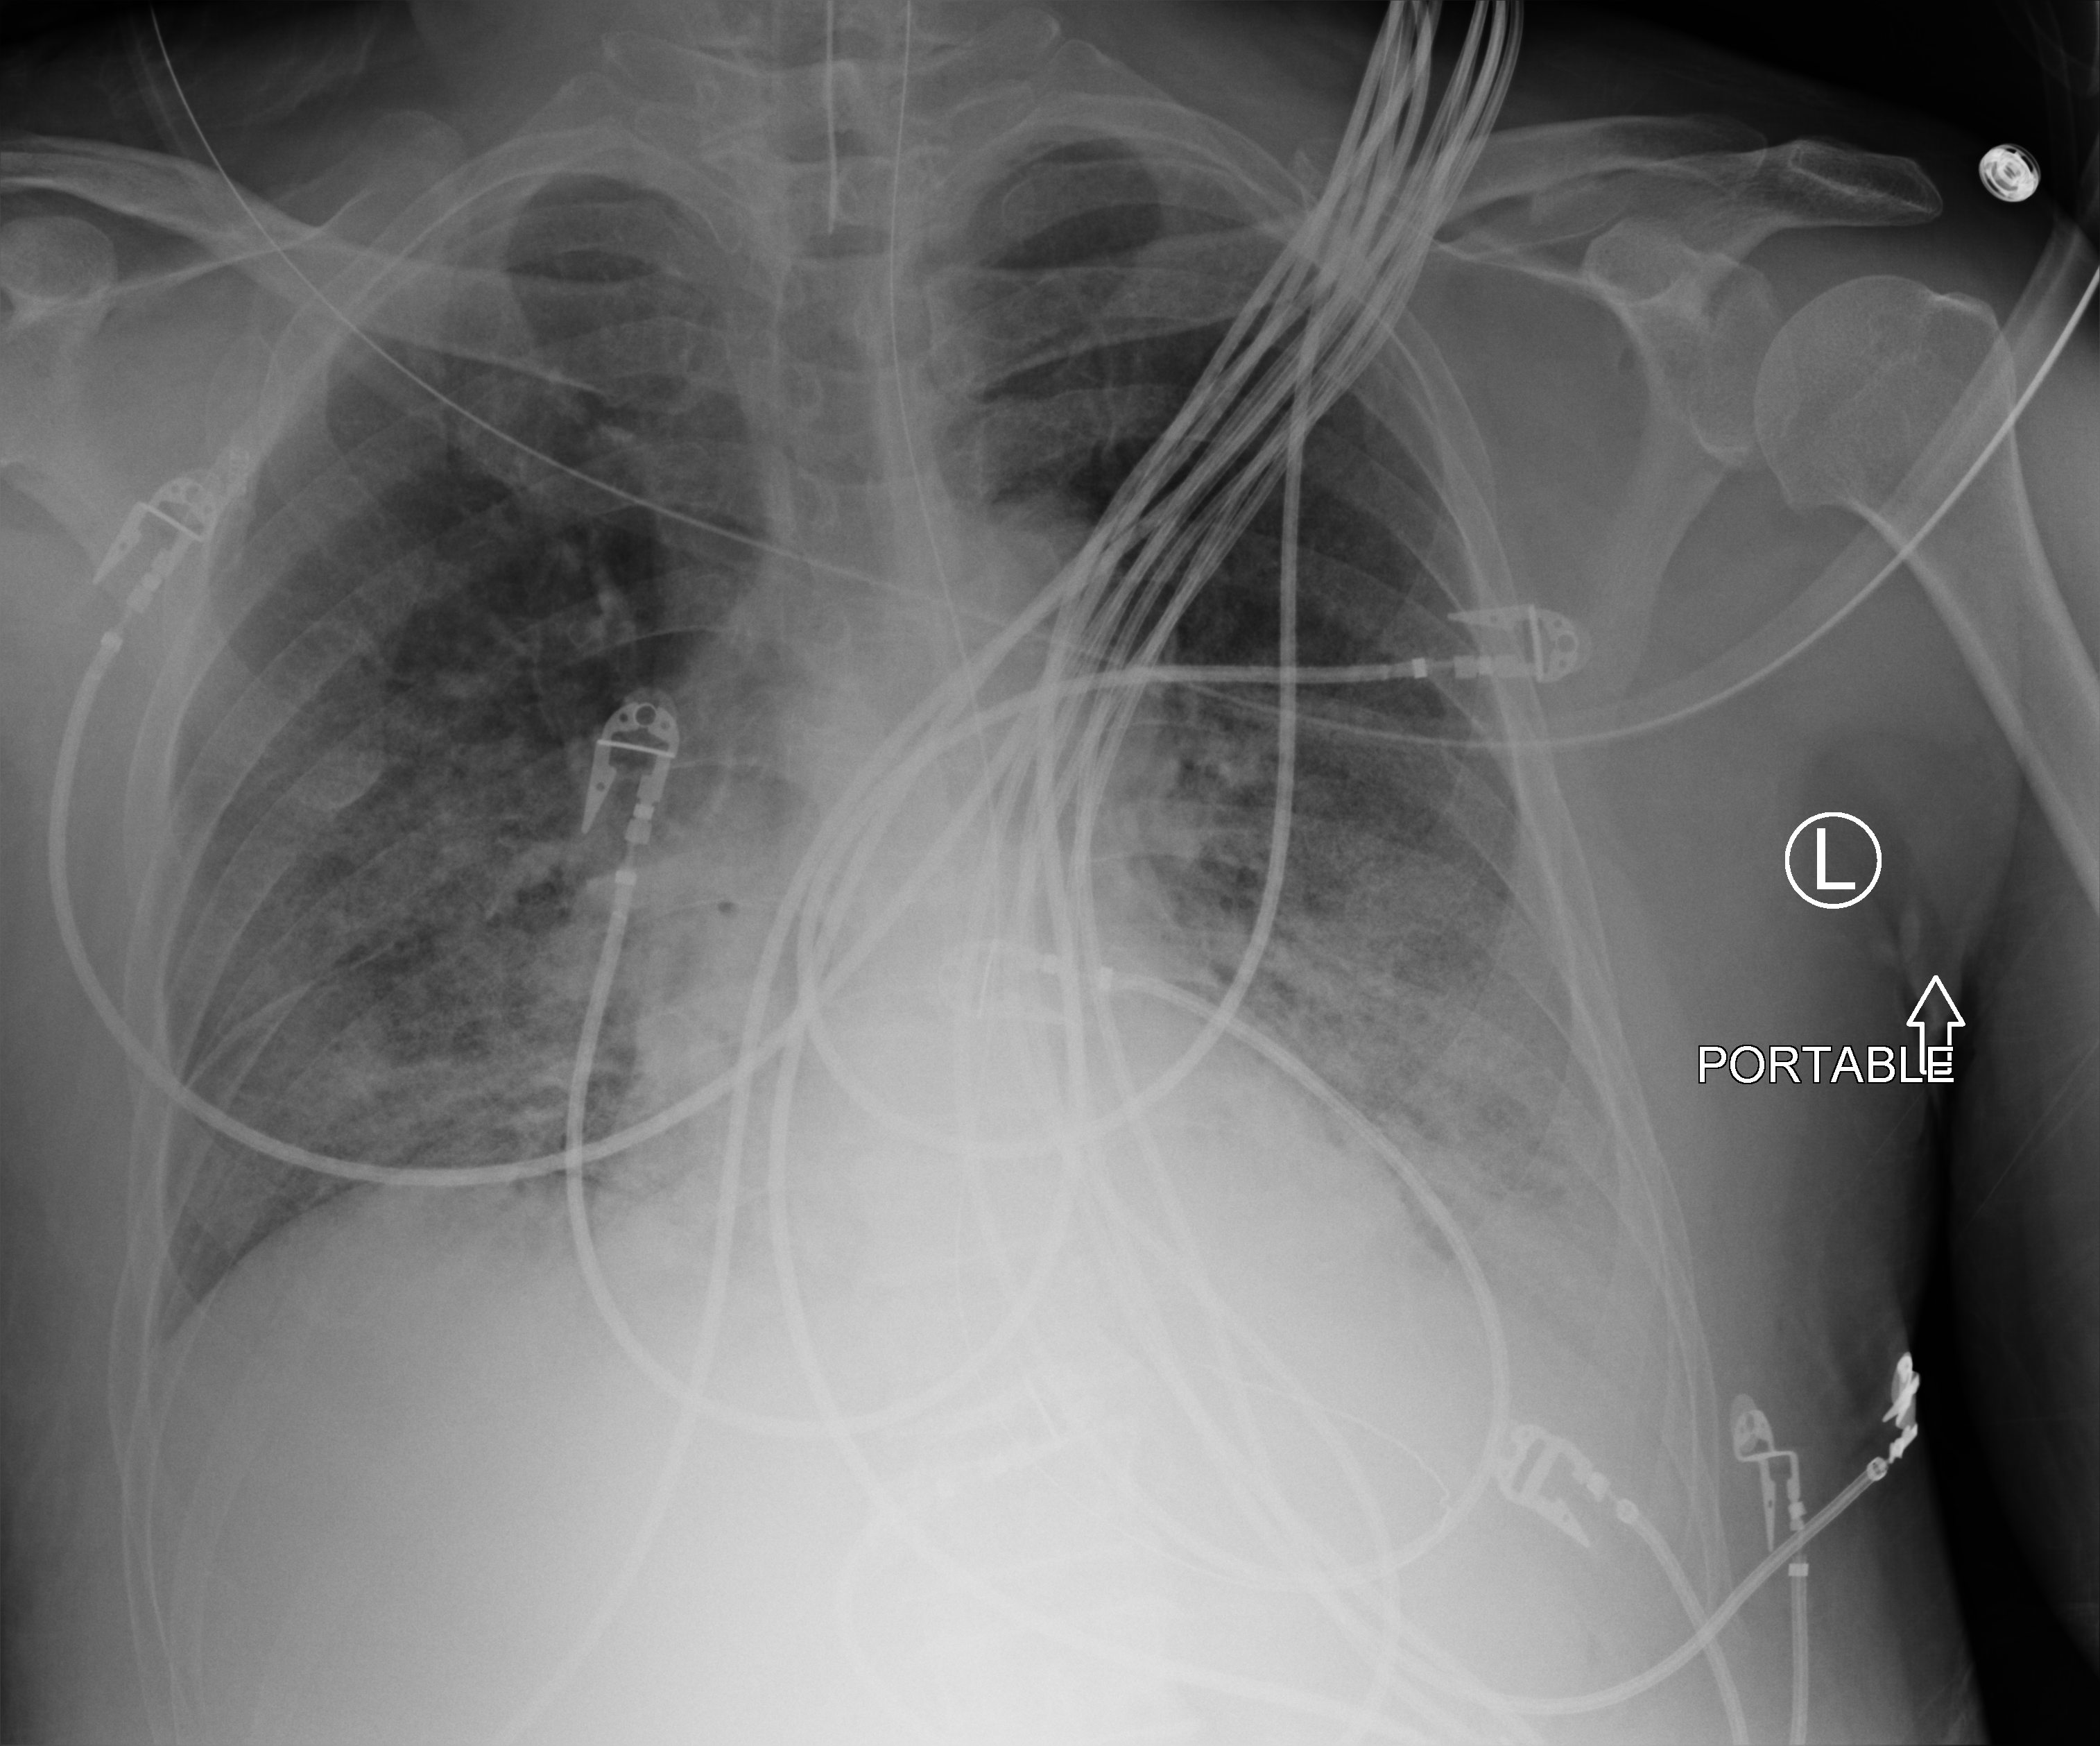
Bedside chest radiograph (computed radiography). Male patient hospitalised with COVID-19, age 60–74 years.
Hospital-stay facts (about this admission, not read from this image; timing relative to this image not recorded): hypertension (admission record): yes; length of hospital stay: 14 days; admitted to intensive care during this hospital stay: yes.